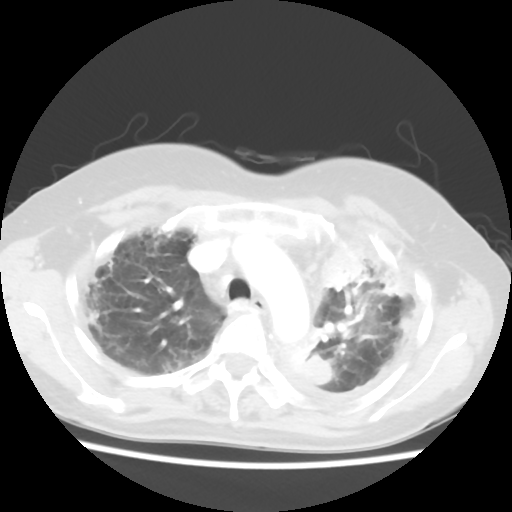
Chest CT, one axial slice; slice 42 of 56 in the series (ordered by position); reconstruction kernel STANDARD; 120 kVp; lung window (W 1500 / L -600 HU); 5 mm slice thickness; 512 × 512 image matrix. Female patient, age 56 years. From the clinical record (not read from this slice): clinical TNM (as recorded): T1c N0 M1.
Annotated regions visible in this slice (bounding box drawn by a radiologist):
- lung tumour (recorded histology: adenocarcinoma): bounding box [x1, y1, x2, y2] px = [320, 235, 370, 299]